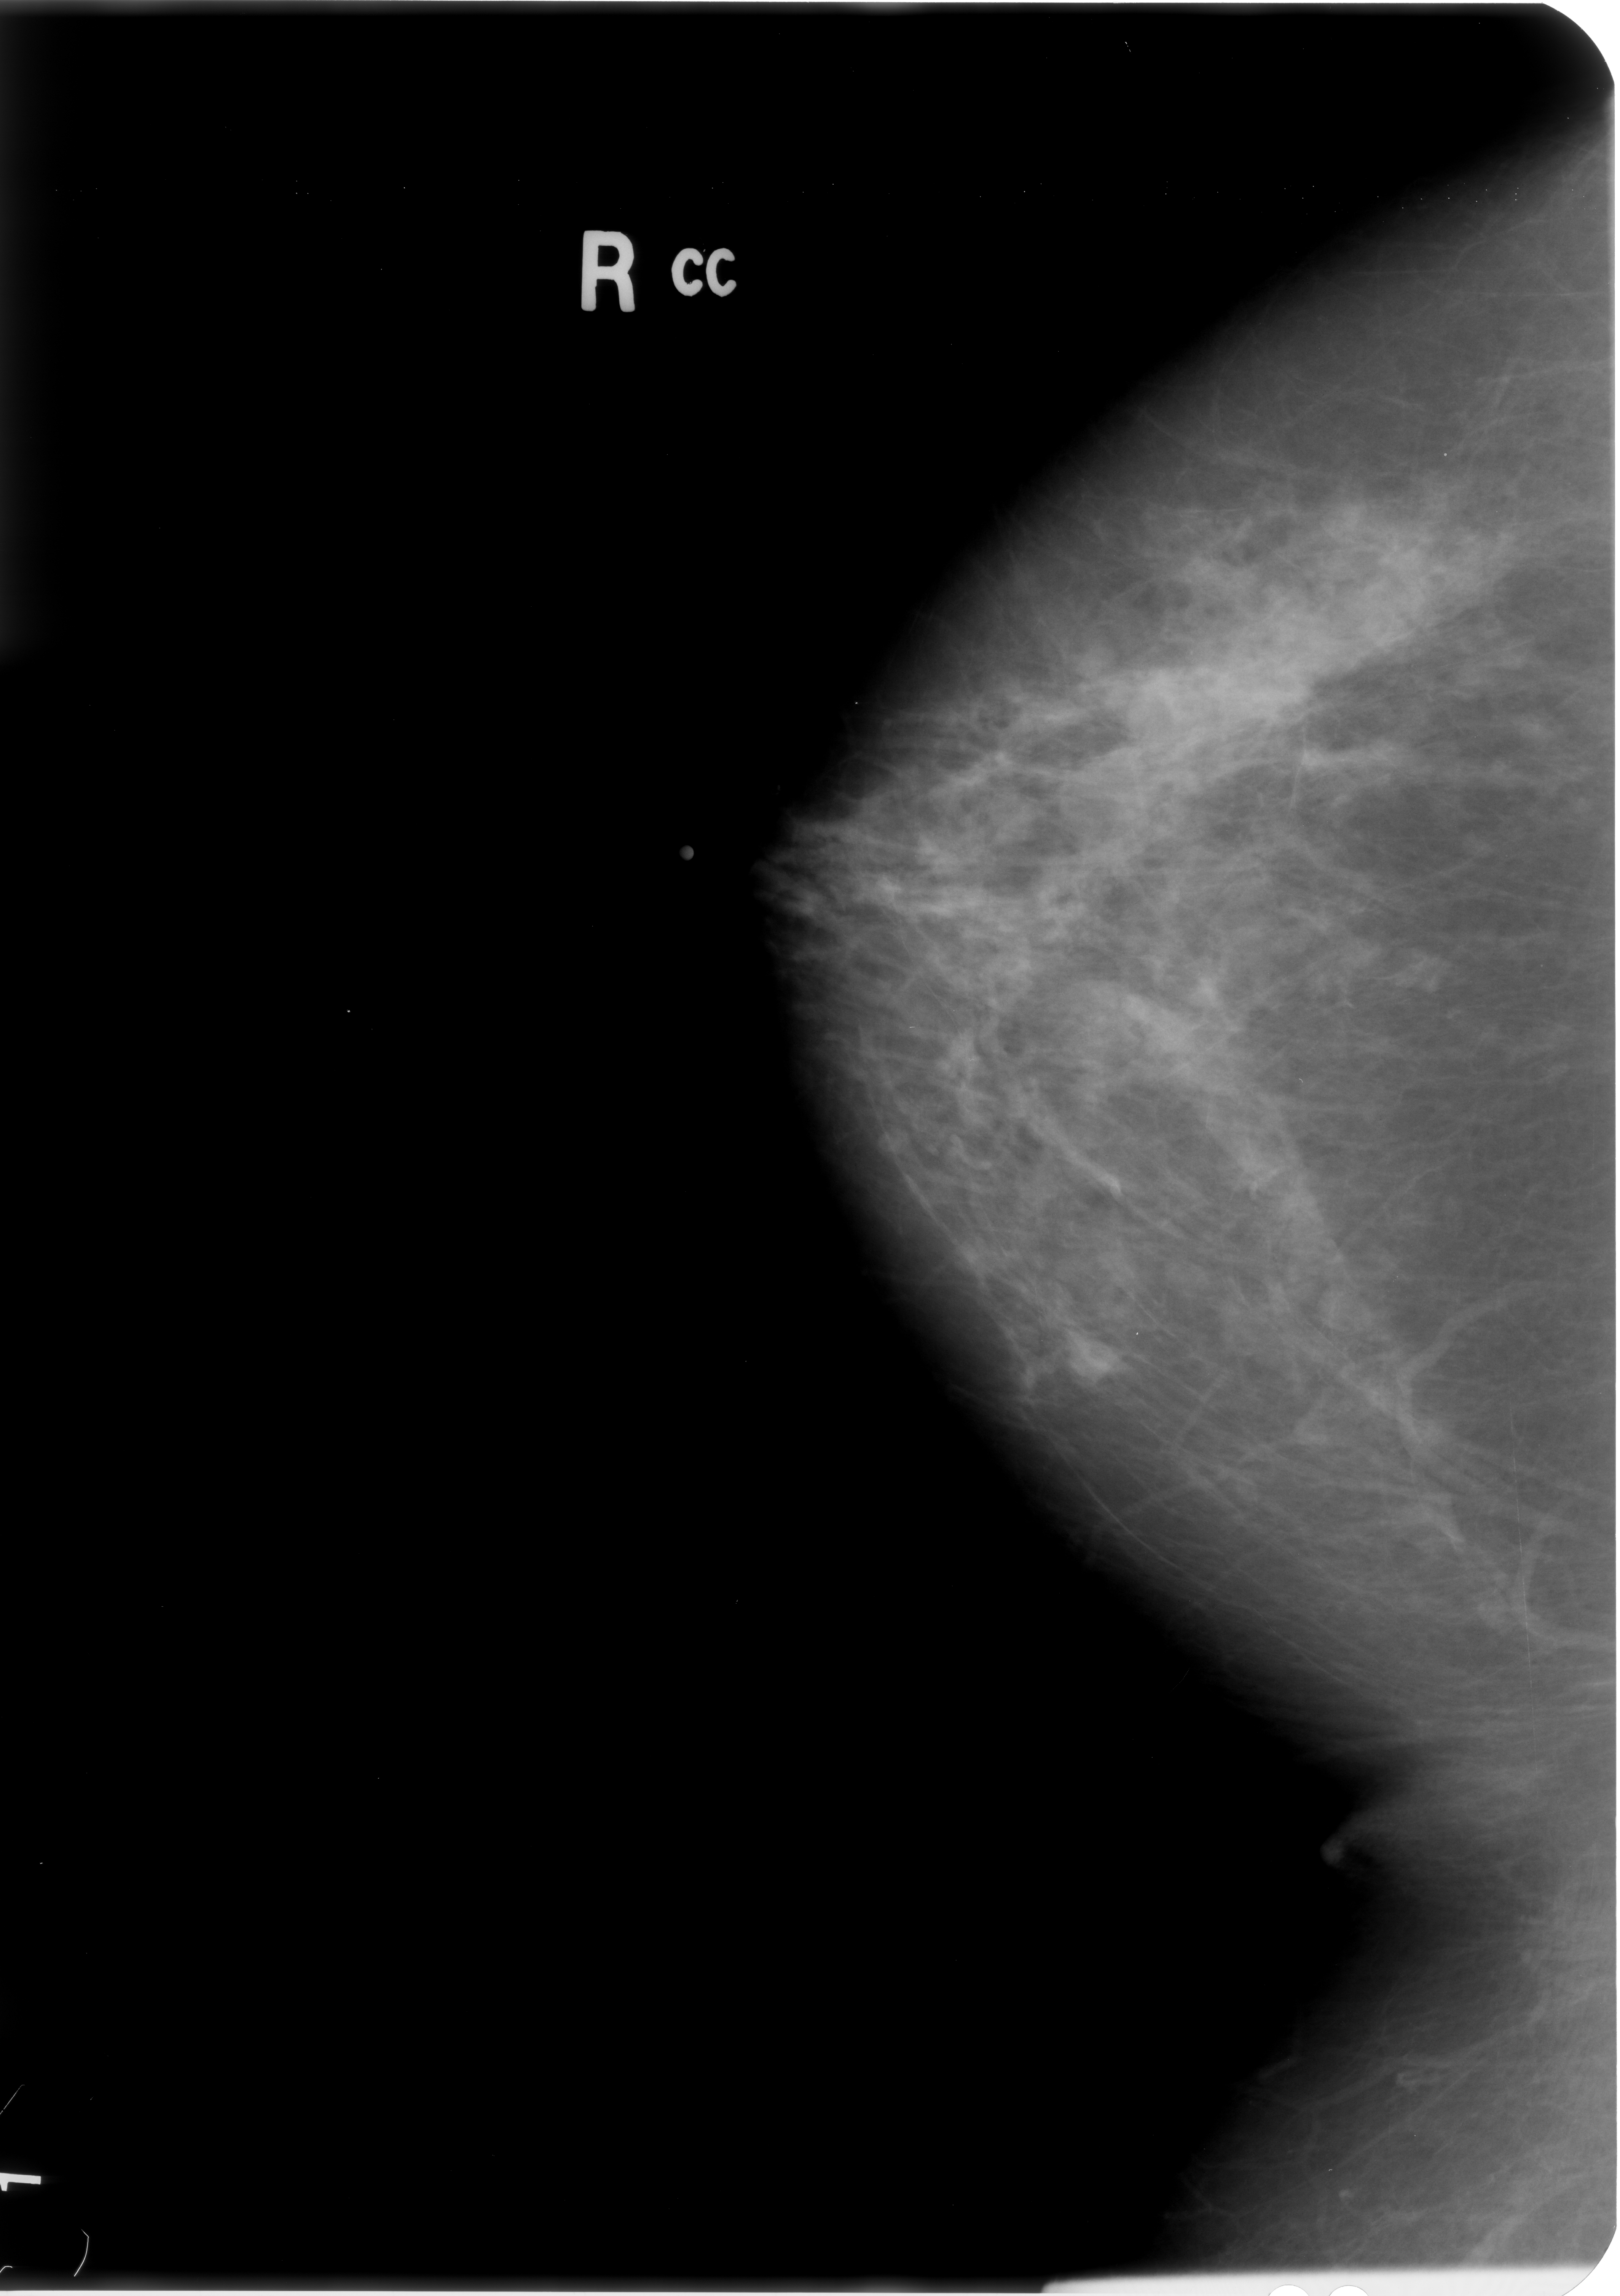
Scanned film-screen mammogram. Right breast. CC view. BI-RADS breast density category 2 (scale 1–4). 1620 × 2296 image matrix.
Expert-marked regions of interest on this image (one box per marked abnormality):
- mass, shape round / lobulated, margins circumscribed; BI-RADS assessment category 3; pathology result (as recorded, not read from the image): benign: bounding box [x1, y1, x2, y2] px = [1120, 664, 1209, 764]